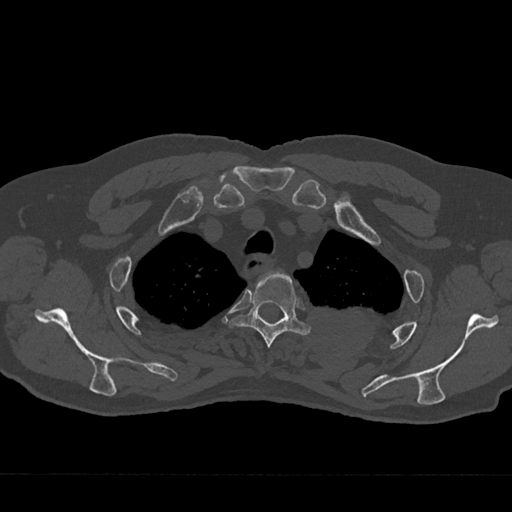
CT including the spine, one axial slice. Slice 572 of 797 in the series (ordered by position). Reconstruction kernel Br40s/3. 120 kVp. Bone window (W 1800 / L 400 HU). 0.5 mm slice thickness. 512 × 512 image matrix. Male patient, age 75 years. Case-level facts recorded for this patient, not image findings: primary cancer: renal; vertebrae with lytic lesions (as recorded): T4.
Structures marked on this image (semi-automatic segmentation, software-assisted and operator-edited):
- T3 vertebra: bounding box <230,271,311,348> (left, top, right, bottom; pixels)